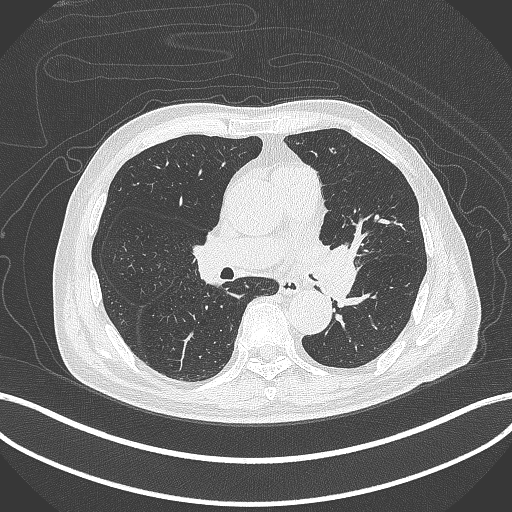
Chest CT, one axial slice; position 232 of 417 along the scan axis; reconstruction kernel B70f; 120 kVp; lung window (W 1500 / L -600 HU); 1 mm slice thickness; 512 × 512 image matrix, field of view 400 × 400 mm. Patient: male, 77 years. Case-level facts recorded for this patient, not image findings: clinical TNM (as recorded): T3 N1 M0.
Annotated regions visible in this slice (rectangle marked by the reading radiologist):
- lung tumour (recorded histology: adenocarcinoma): bounding box (x1, y1, x2, y2) in pixels: (306, 235, 359, 305)